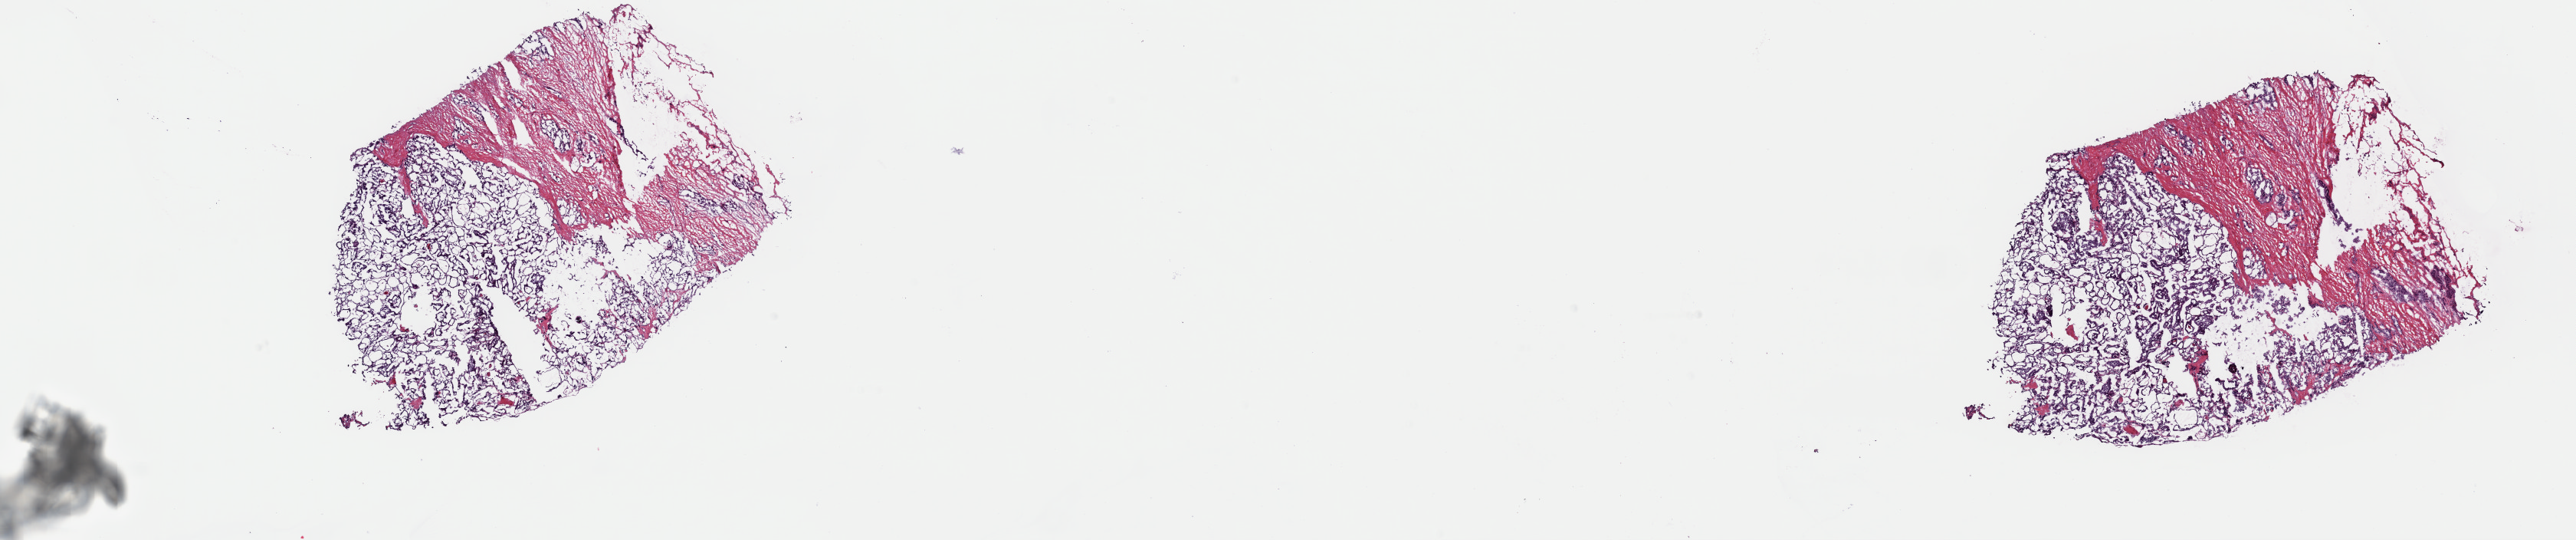
Digitized Hematoxylin and eosin (H&E) stained tissue section (whole slide) — low-resolution overview of the scanned area, about 26.5 x 5.6 mm (from a 40x scan); frozen section from the top of the tissue portion; thyroid, primary tumour sample. Female patient; age at initial diagnosis 47 years. Pathologist review of this section (percent, as recorded): tumour cells 60%, tumour nuclei 90%, normal cells 0%, stromal cells 40%, necrosis 0%. Infiltration values recorded for this section: lymphocyte infiltration 1%, monocyte infiltration 0%, neutrophil infiltration 0%.
* AJCC pathologic stage: III
* lymph nodes positive (case pathology): 7 of 20 examined
* laterality: right
* diagnosis: Papillary adenocarcinoma, NOS (thyroid gland)